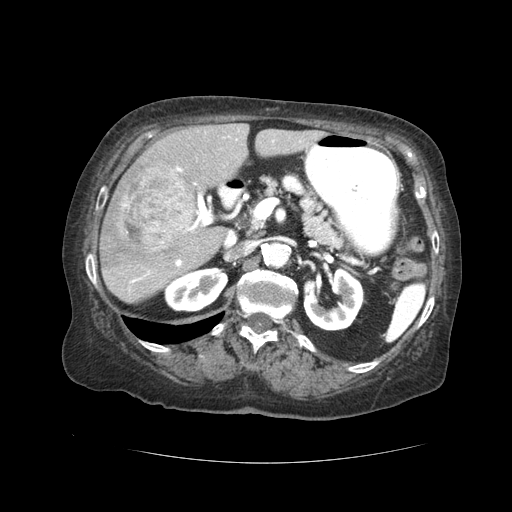
Contrast-enhanced abdominal CT (liver protocol), one axial slice. Slice 17 of 59 in the series (ordered by position). Reconstruction kernel STANDARD. 120 kVp. Soft-tissue window (W 400 / L 40 HU). 512 × 512 image matrix, field of view 380 × 380 mm. Case-level facts recorded for this patient, not image findings: diagnosis: hepatocellular carcinoma (patient treated with transarterial chemoembolisation; whether this scan precedes or follows treatment is not stated here); TNM stage (as recorded): Stage-I; Child-Pugh class: A; tumour nodularity: uninodular.
Outlined on this slice (semi-automatically segmented with operator editing):
- liver parenchyma outside the tumour (the mass and vessels are separate outlines, so this box may not span the whole liver): bounding box (x1, y1, x2, y2) in pixels: (100, 124, 322, 304)
- mass: (111, 171, 197, 249)
- liver vessels: (129, 130, 275, 290)